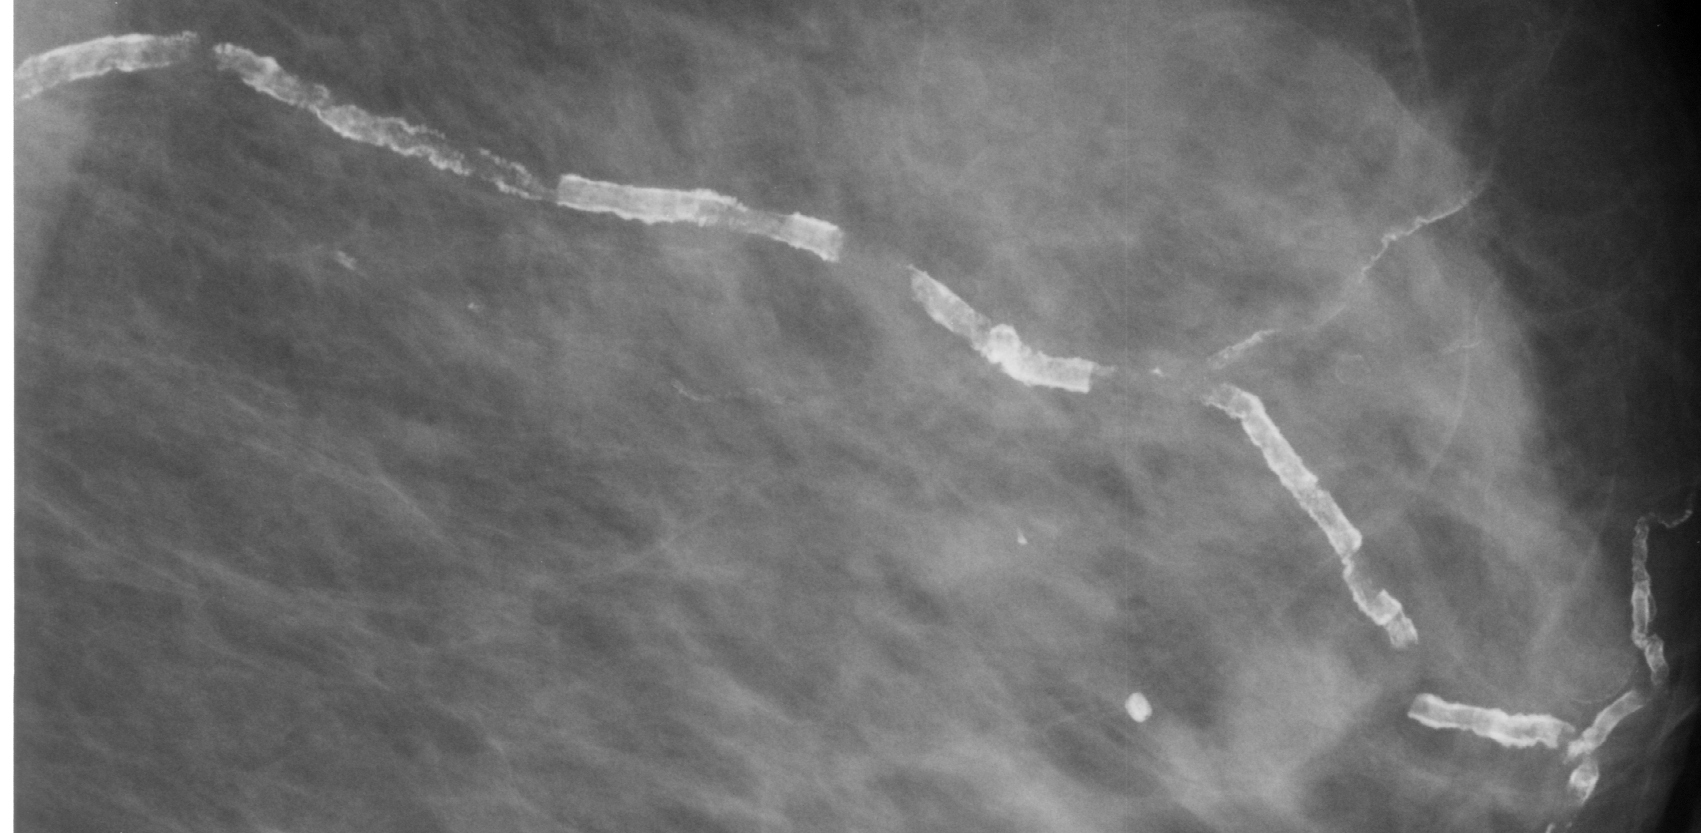
Crop from a digitized film mammogram around one marked abnormality; left breast; MLO view.
Finding: calcifications, morphology vascular; BI-RADS assessment category 2; subtlety rating 5 on a 1 (subtle) to 5 (obvious) scale; benign without callback (not worked up further).